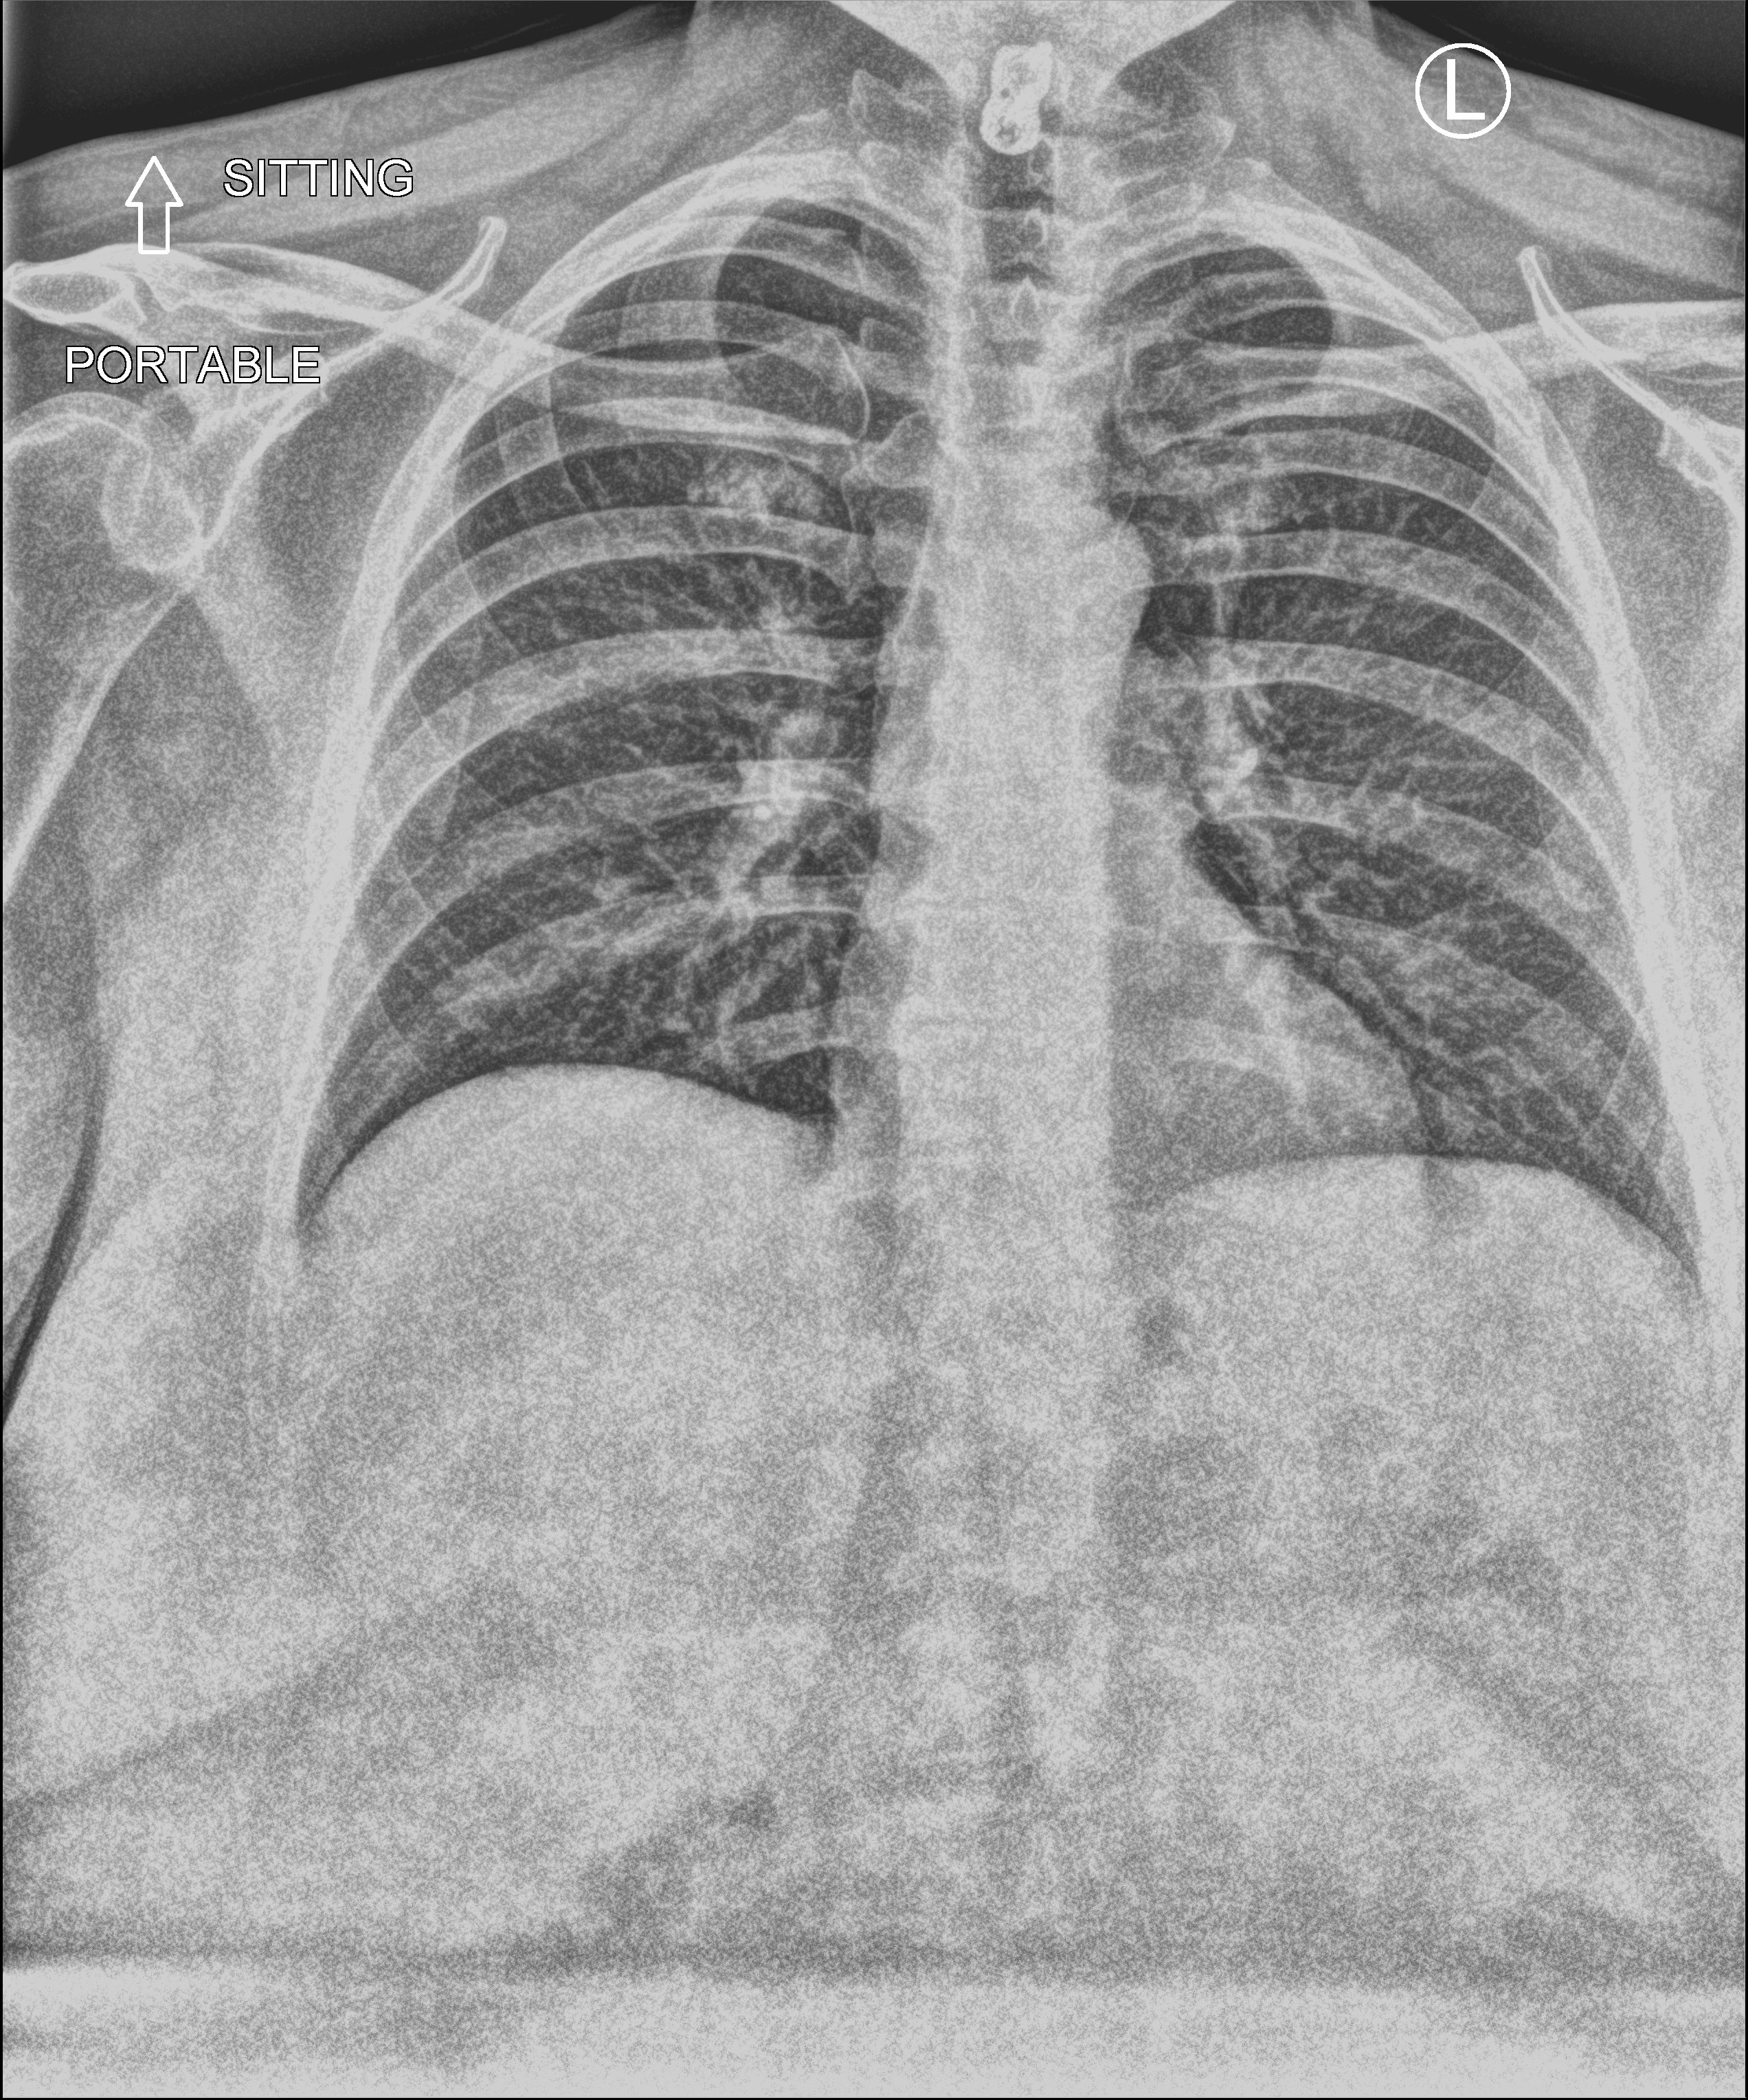
Chest X-ray (portable), anteroposterior (AP) projection. Female patient hospitalised with COVID-19, age 18–59 years.
Hospital-stay facts (about this admission, not read from this image; timing relative to this image not recorded): admitted to intensive care during this hospital stay: no.